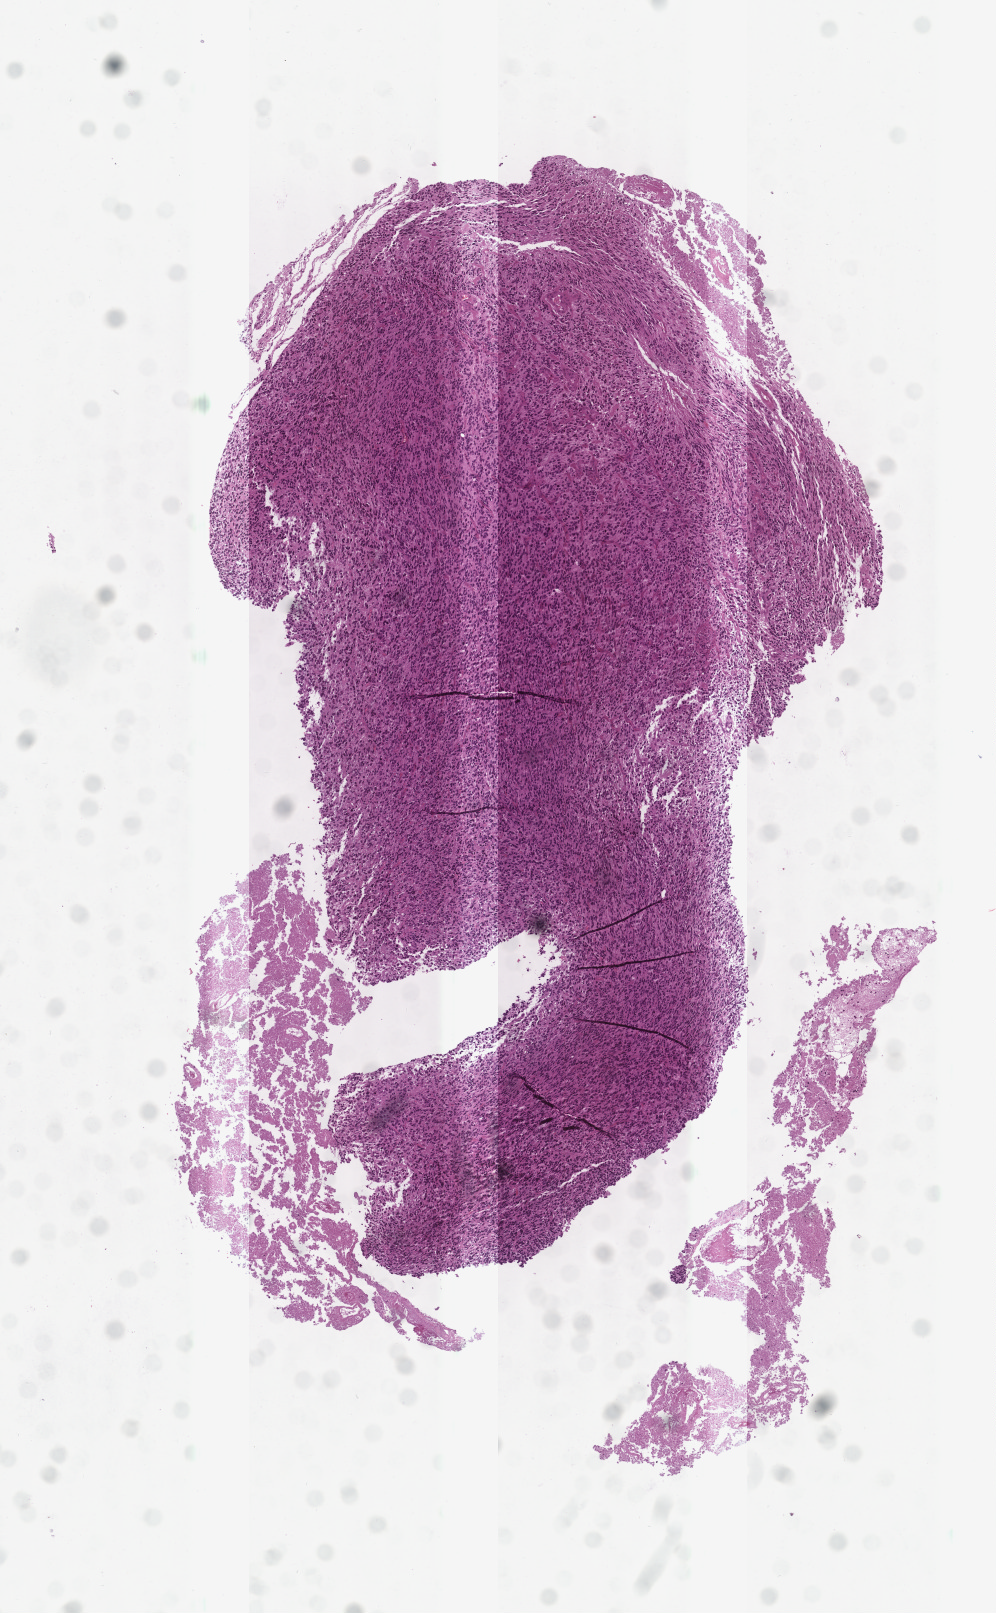
Hematoxylin and eosin (H&E) stained whole-slide image — shown as a low-resolution overview of the whole scanned area (about 4.0 x 6.5 mm, from a 20x scan). Tumour tissue sample, sampled site: brain. Male, 44 y/o. Composition of this section per pathologist review: tumour nuclei 90%, necrosis 10%.
Diagnosis: Glioblastoma.